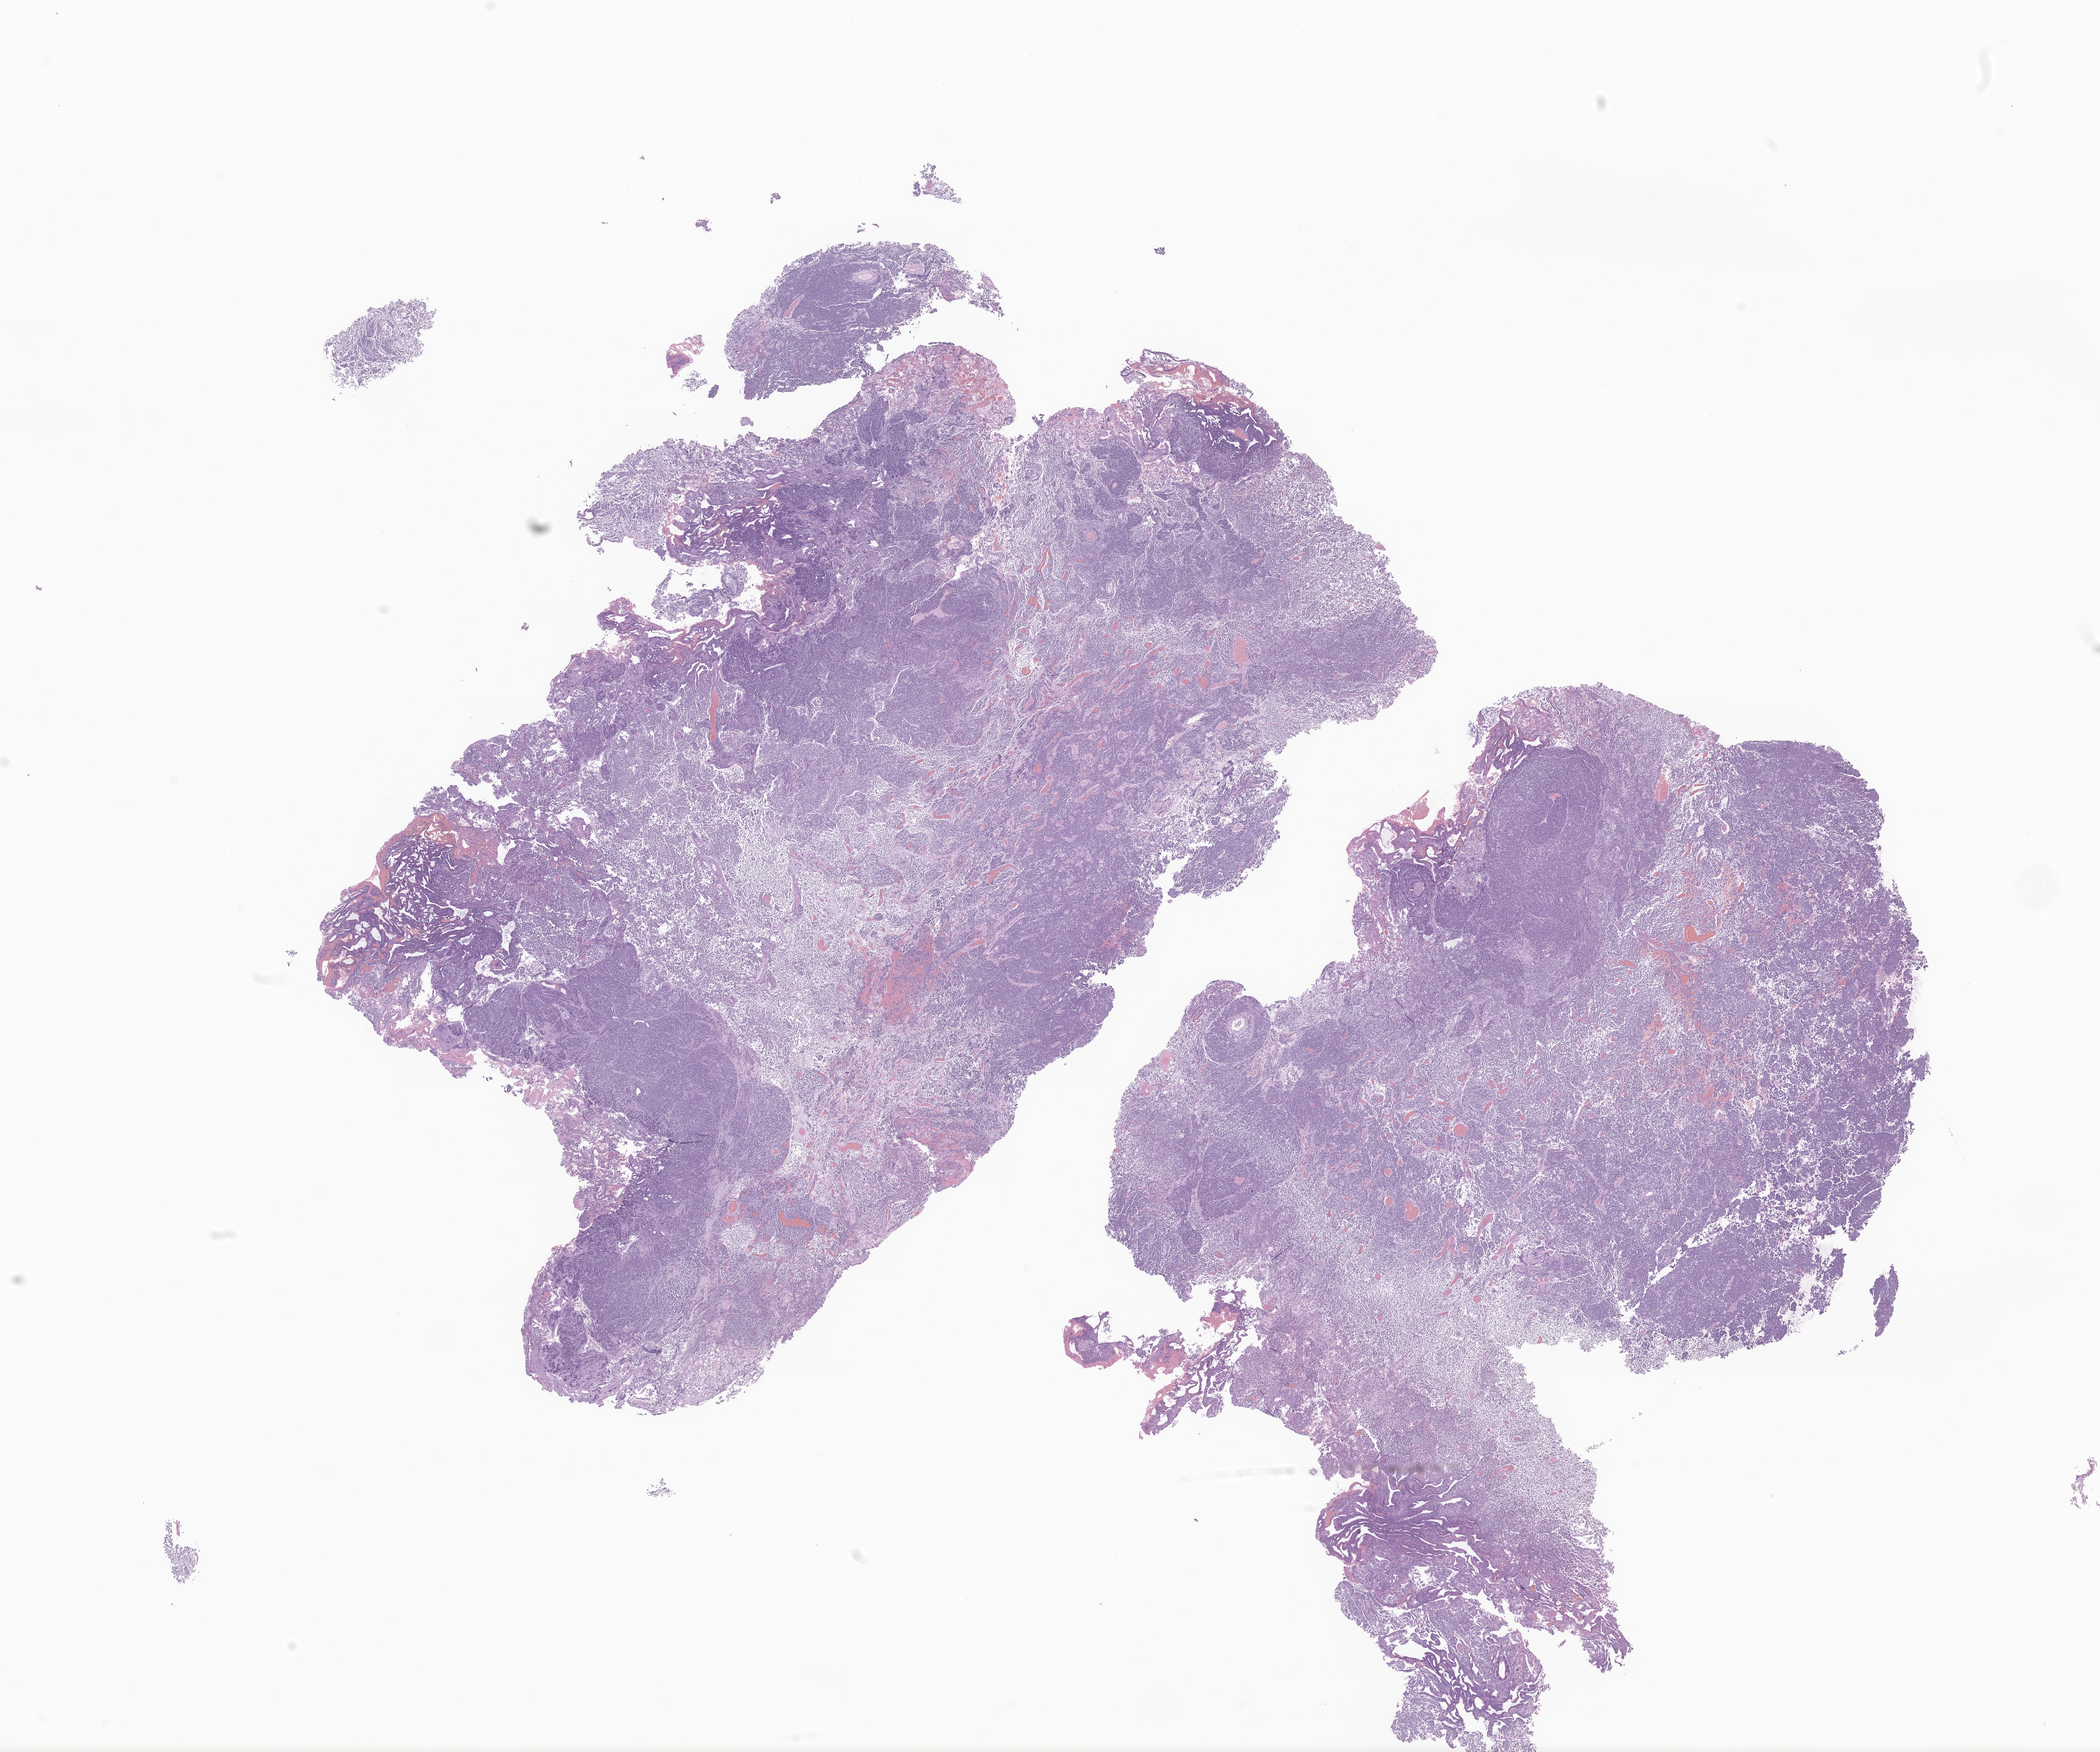
Hematoxylin and eosin (H&E) whole-slide image of tumor tissue from the cerebellum — low-resolution overview of the scanned area, about 23.4 x 19.6 mm, formalin-fixed paraffin-embedded section. Patient female; age 653 days (about 1.8 years).
Recorded diagnosis: Medulloblastoma, NOS.